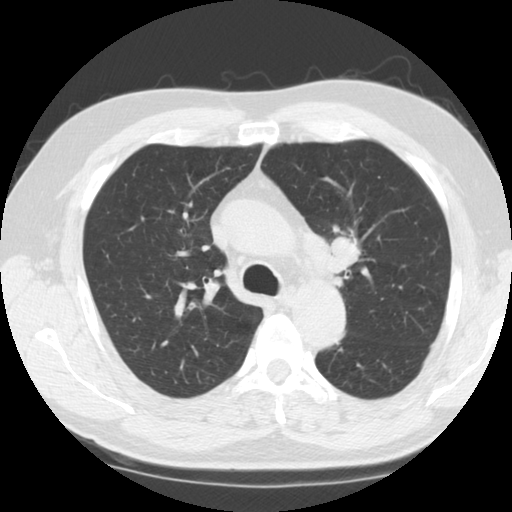
Low-dose screening chest CT, one axial slice; slice 88 of 124 in the series (ordered by position); reconstruction kernel STANDARD; 120 kVp; lung window (W 1500 / L -600 HU); 2.5 mm slice thickness; 512 × 512 image matrix, field of view 340 × 340 mm.
Annotated regions visible in this slice (expert manual segmentation):
- lesion 1 (tumor, upper lobe of left lung): bounding box (x1, y1, x2, y2) in pixels: (326, 235, 364, 274)